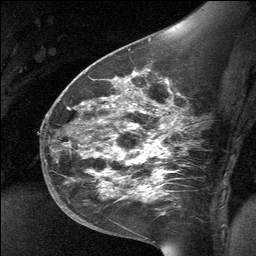
Breast MRI (dynamic contrast-enhanced), one sagittal slice. Slice 39 of 64 in the series (ordered by position). Dynamic contrast-enhanced study with each time point stored as its own series, time point 2 of 3 at this slice position (early post-contrast, ordered by acquisition time). 1.5 T. TE 4.8 ms, TR 27 ms. 256 × 256 image matrix, field of view 200 × 200 mm. Patient: female, 39 years. Case-level facts recorded for this patient, not image findings: setting: breast cancer imaged before/during neoadjuvant chemotherapy; receptor status: HER2-positive.
Outlined on this slice (semi-automatic segmentation, software-assisted and operator-edited):
- analysis volume of interest (the breast-tissue region the enhancement analysis was run in; not a lesion): bounding box (x1, y1, x2, y2) in pixels: (70, 69, 186, 224)
- tumour enhancement mask (voxels above the 90 % enhancement threshold inside the analysis volume of interest): (105, 124, 160, 192)